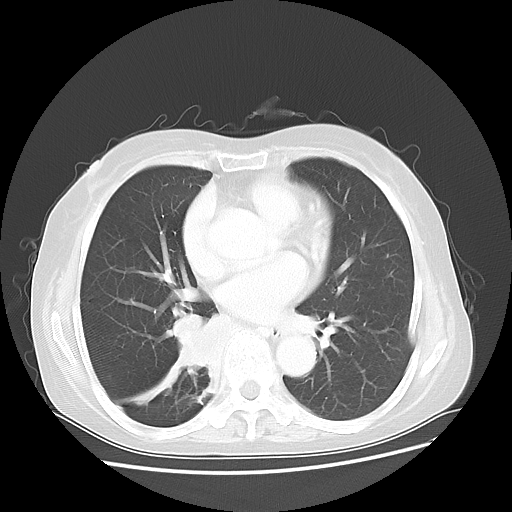
Chest CT, one axial slice. Slice 21 of 47 in the series (ordered by position). Reconstruction kernel LUNG. 120 kVp. Lung window (W 1500 / L -600 HU). 512 × 512 image matrix. Female patient, age 63 years. From the clinical record (not read from this slice): clinical TNM (as recorded): T2 N3 M1b; histopathological grade: G3.
Structures marked on this image (bounding box drawn by a radiologist):
- lung tumour (recorded histology: small cell carcinoma): bounding box <161,312,236,386> (left, top, right, bottom; pixels)